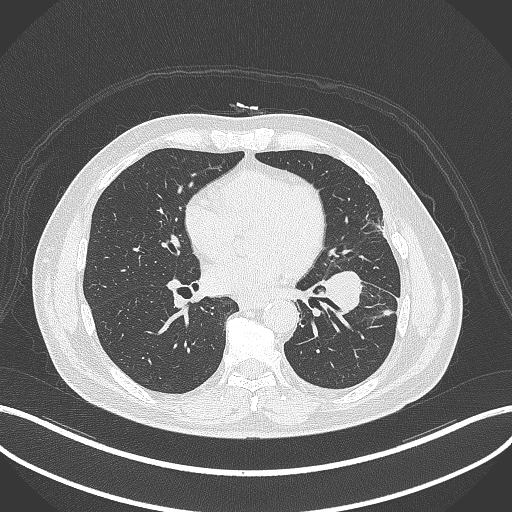
Chest CT, one axial slice. Position 161 of 230 along the scan axis. Reconstruction kernel B70f. 120 kVp. Lung window (W 1500 / L -600 HU). 512 × 512 image matrix. Male patient, age 68 years. Case-level facts recorded for this patient, not image findings: clinical TNM (as recorded): T2b N0 M0.
Annotated regions visible in this slice (rectangle marked by the reading radiologist):
- lung tumour (recorded histology: squamous cell carcinoma): bounding box <321,266,367,314> (left, top, right, bottom; pixels)